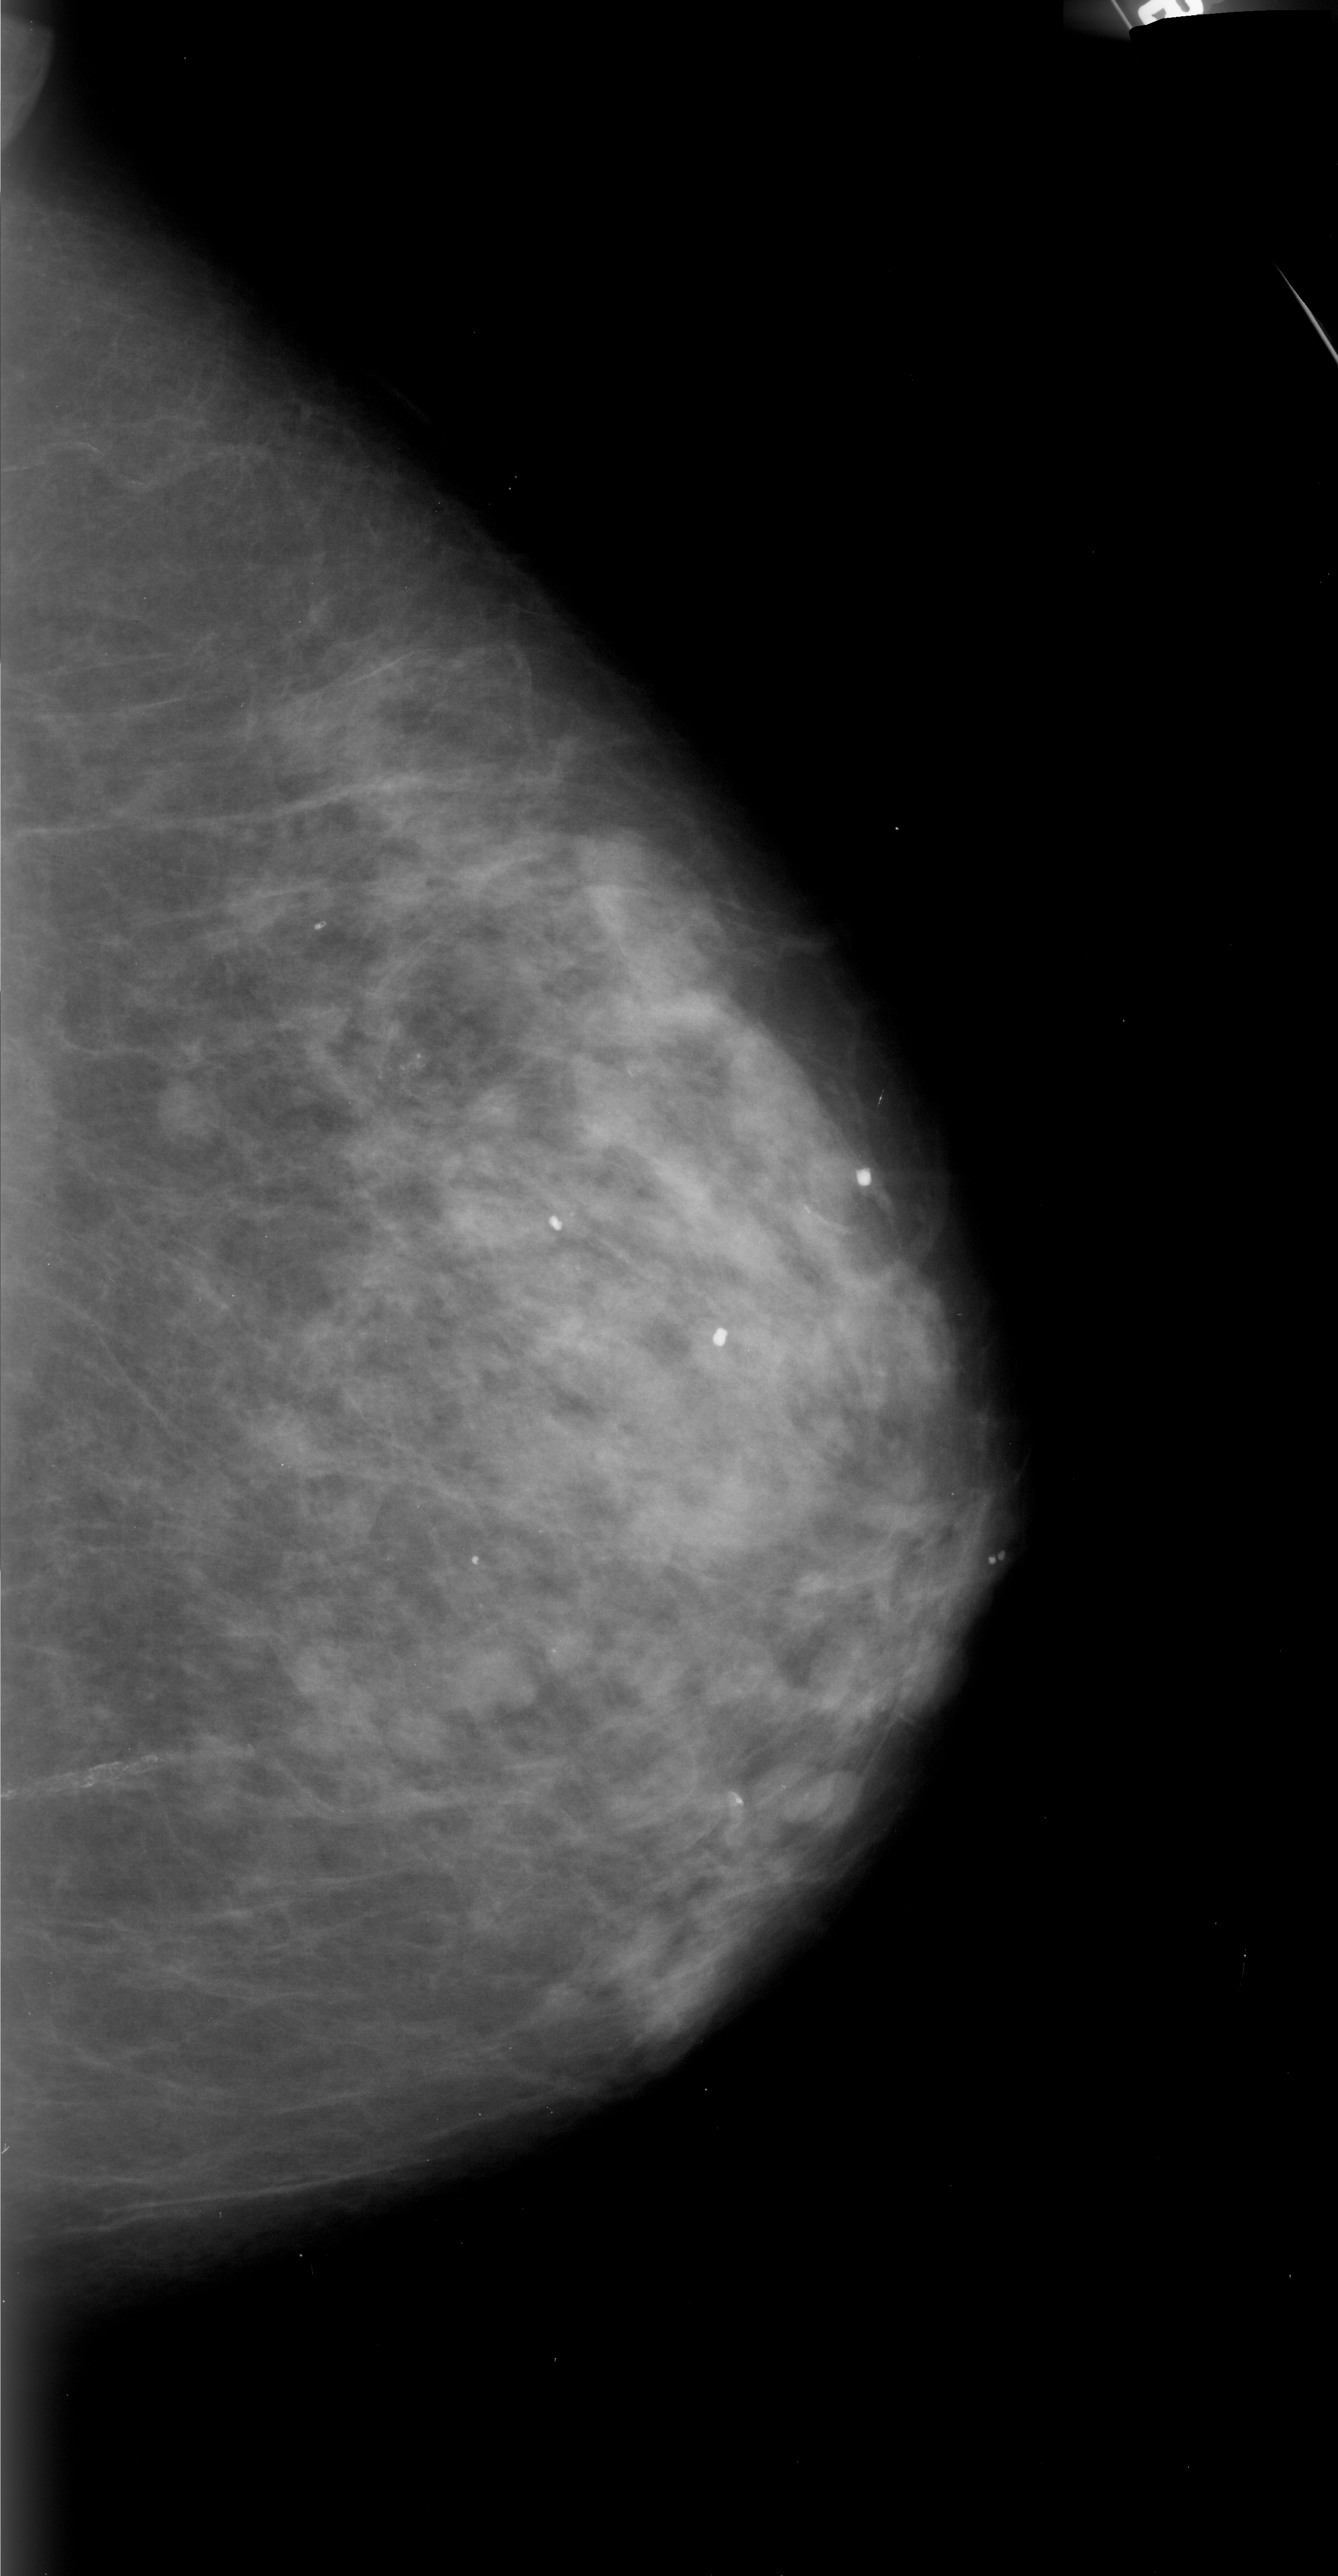
Mammogram (digitized film); right breast; CC view; breast composition: heterogeneously dense (BI-RADS density category 3 of 4); 1338 × 2576 image matrix.
Expert-marked regions of interest on this image (one box per marked abnormality):
- calcifications, morphology pleomorphic, distribution clustered; BI-RADS assessment category 4; pathology result (as recorded, not read from the image): malignant: bounding box [x1, y1, x2, y2] px = [362, 1030, 458, 1118]